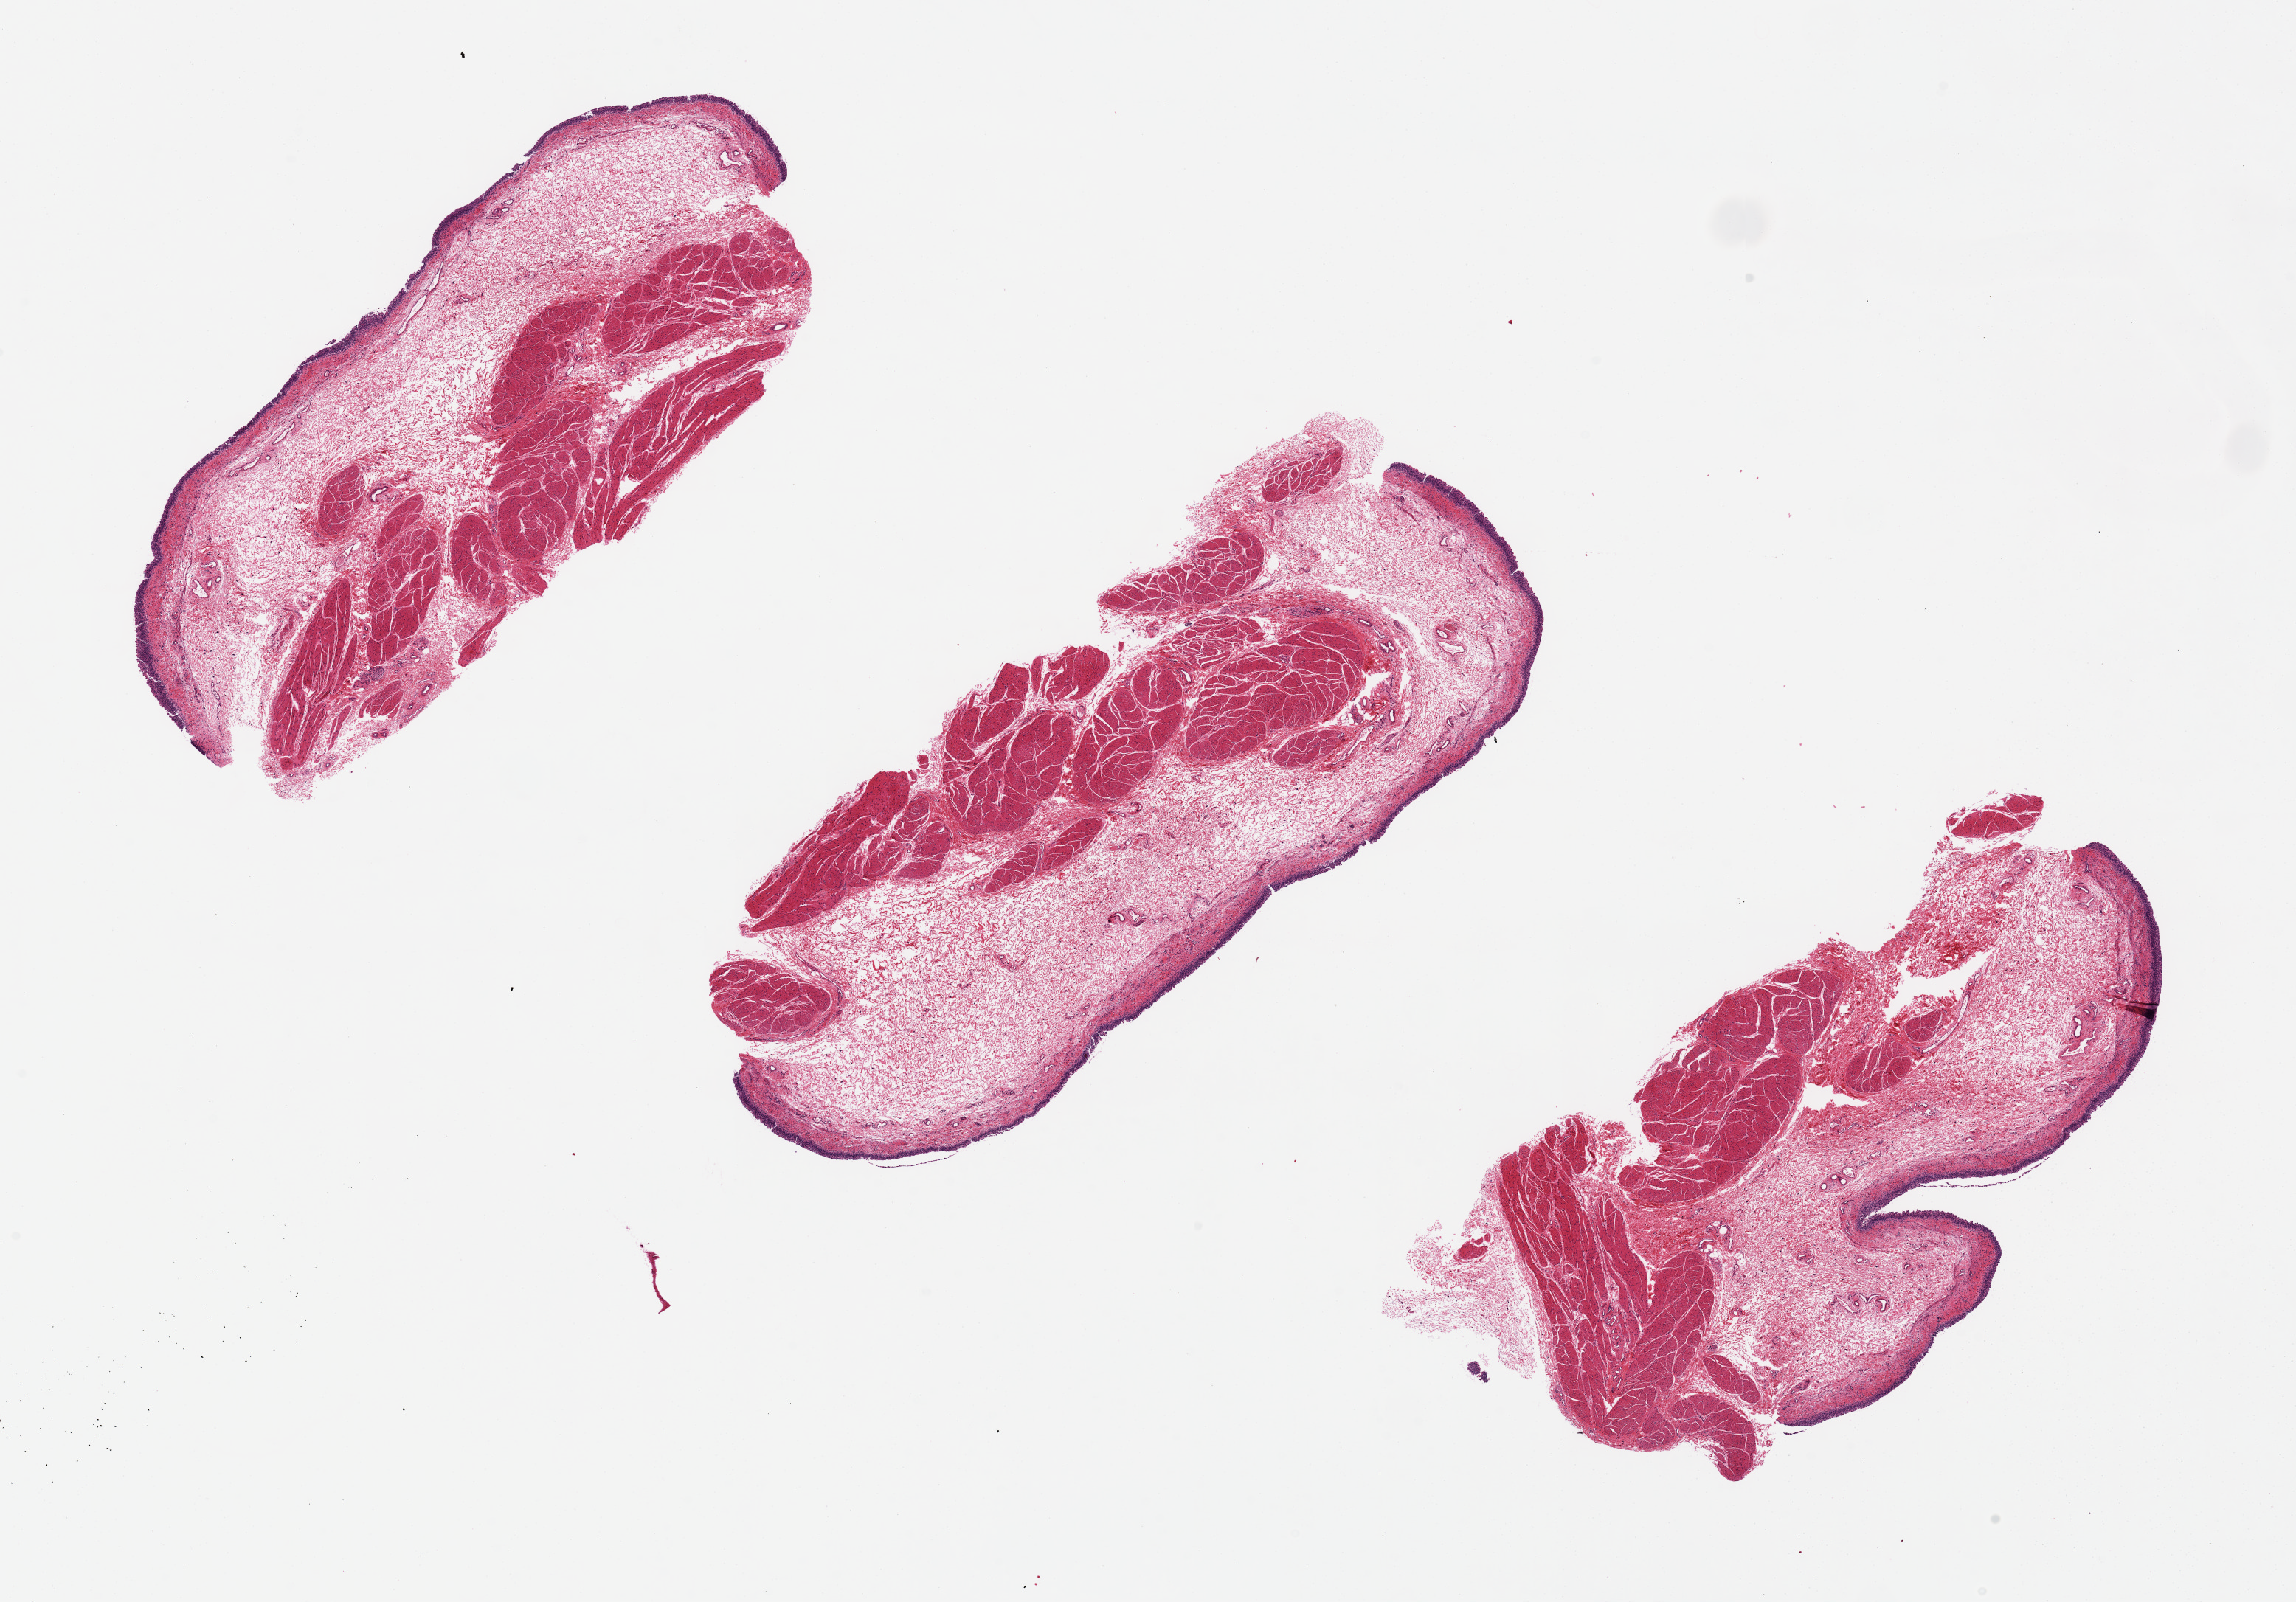
Whole-slide image, haematoxylin and eosin stain — shown as a low-resolution overview of the whole scanned area (about 24.6 x 17.2 mm); PAXgene-fixed paraffin-embedded (PFPE) section; sampled site (target tissue): urinary bladder; tissue donor sample. Donor sex: male.
* review note (as recorded): 1. 10 x 4mm pieces (3); urothelium remarkably well preserved, up to 6-70 microns thick